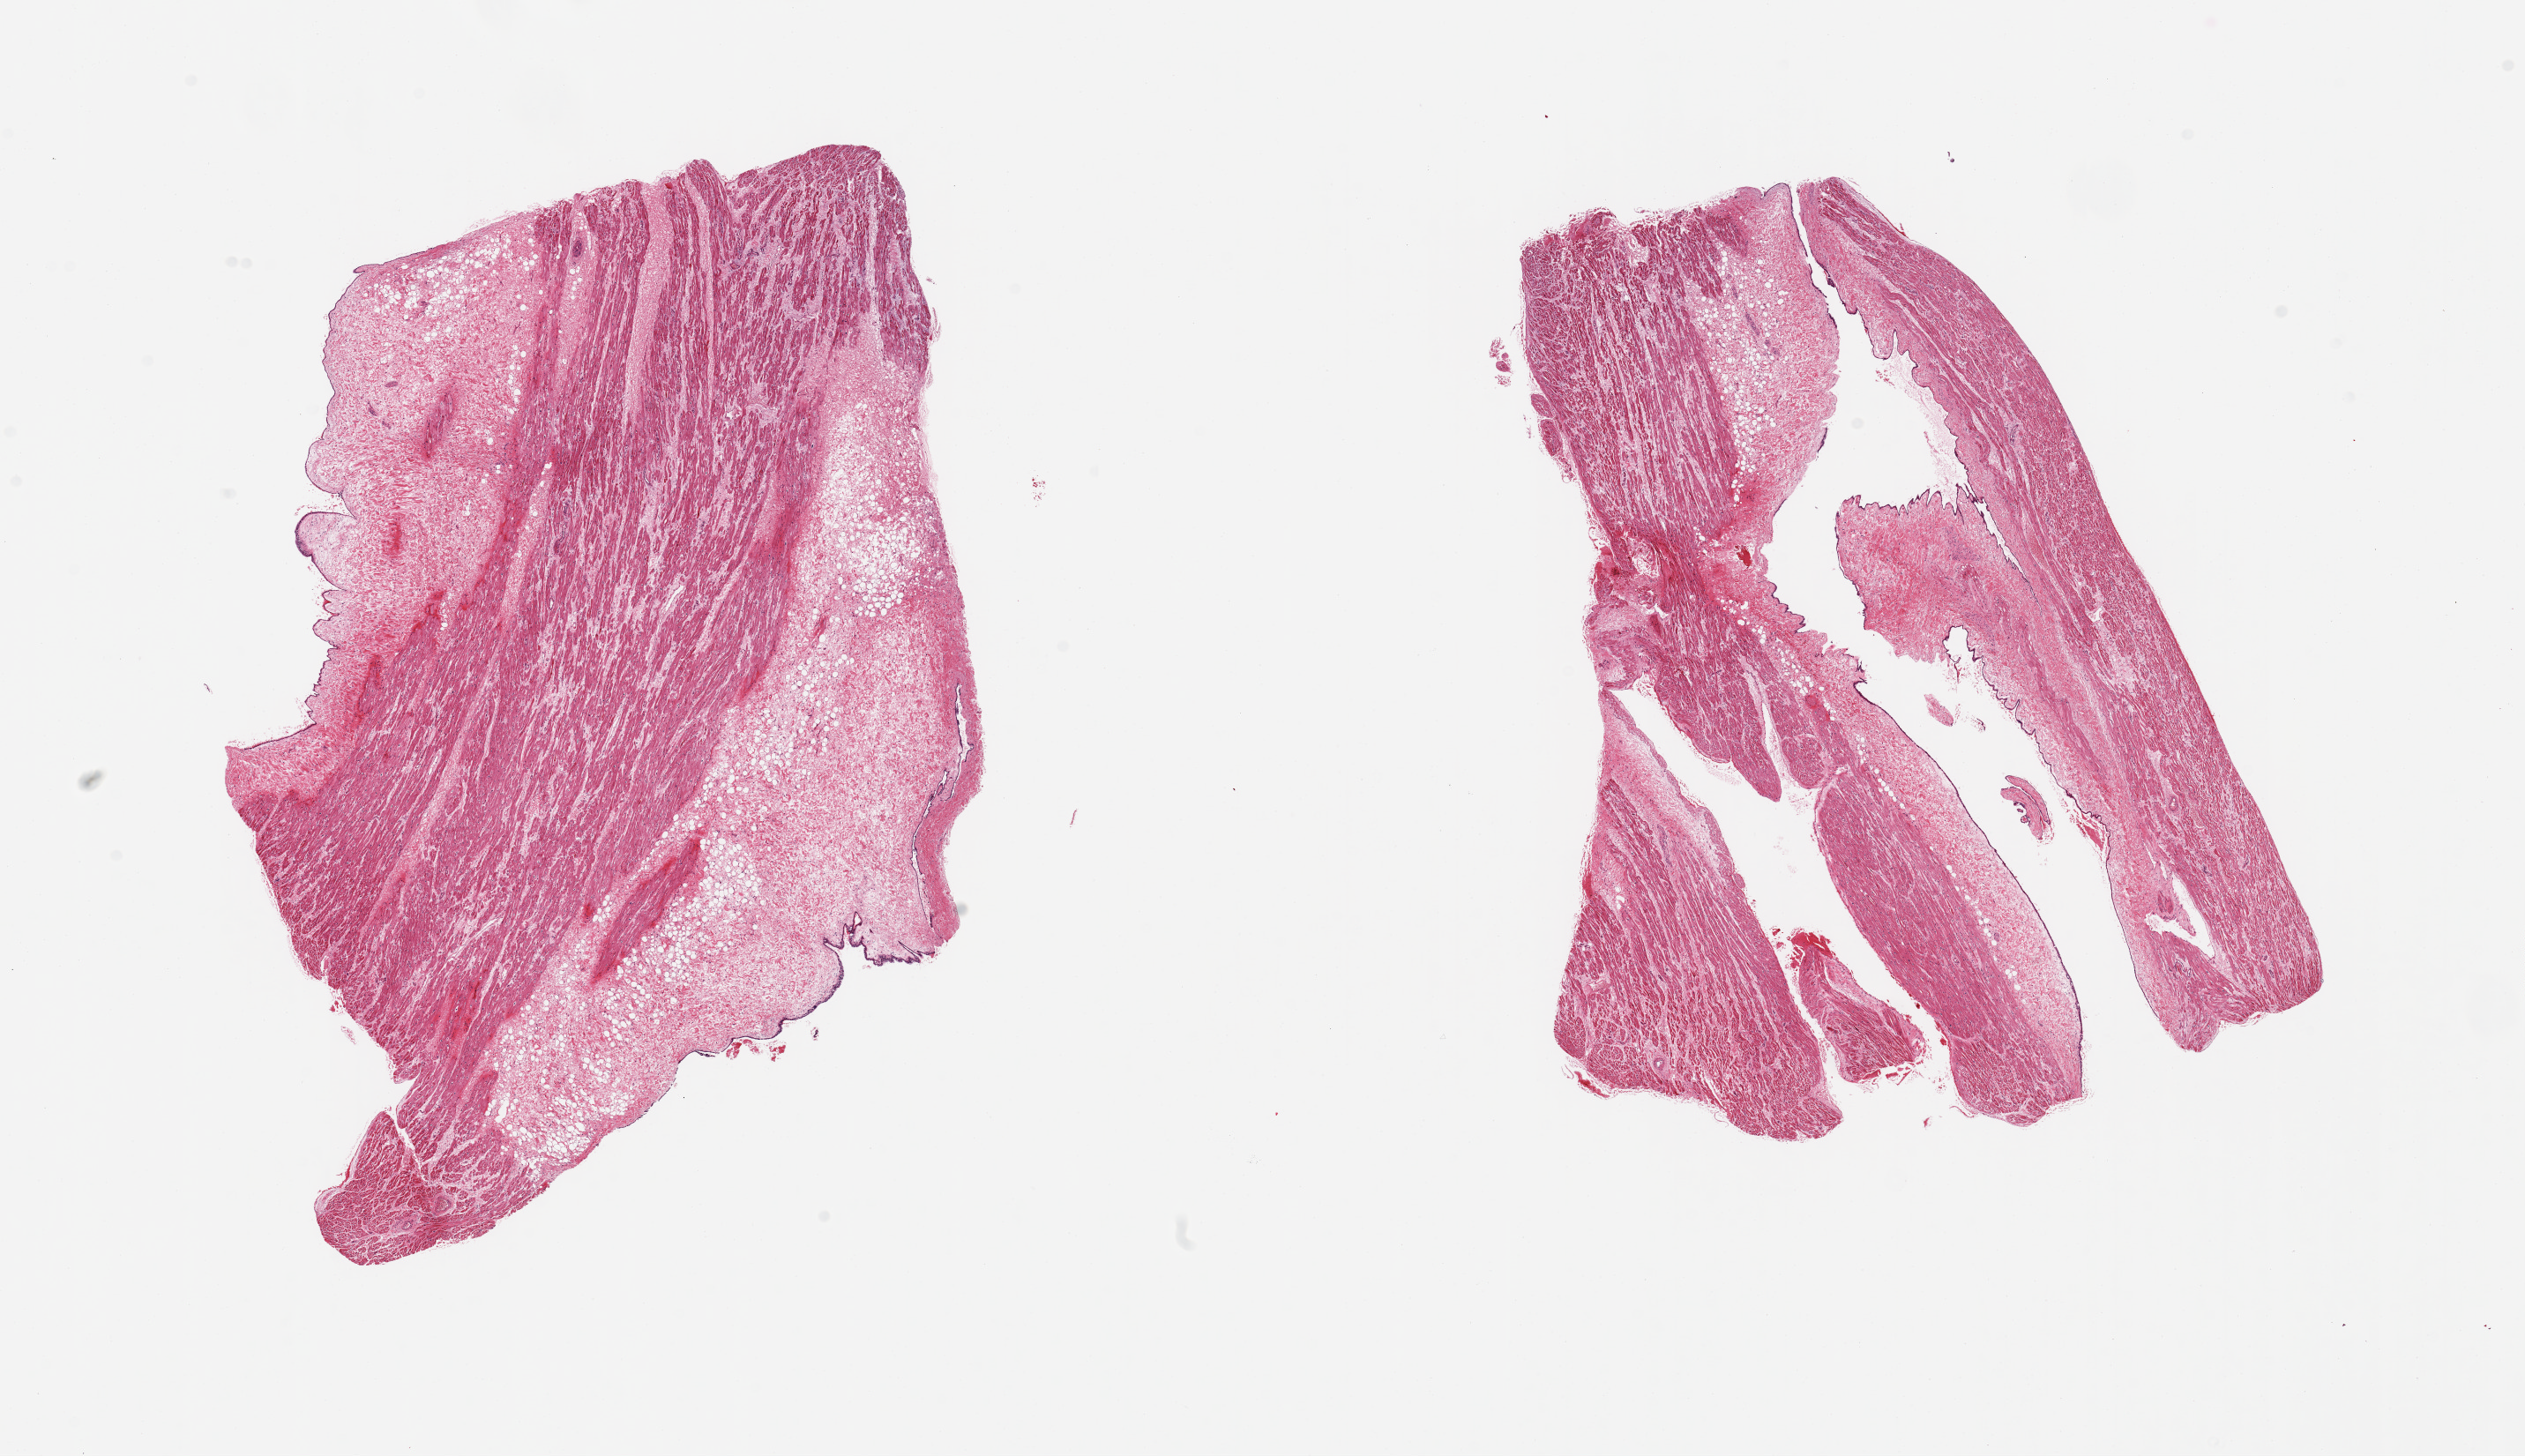
Hematoxylin and eosin (H&E) whole-slide image, a low-resolution overview of the entire scanned area, about 22.6 x 13.1 mm (slide scanned at 20x); PAXgene-fixed paraffin-embedded (PFPE) section; sampled site (target tissue): auricular appendage; donor tissue sample.
Pathologist's review note for this sample: 2 pieces; ~ 20% and 50% internal fat and fibrous tissue, patchy wavy fibers and contraction bands.